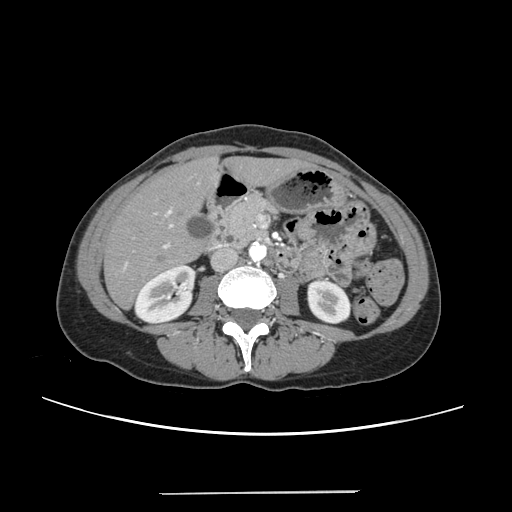
Contrast-enhanced abdominal CT, one axial slice. 120 kVp. Intravenous contrast given. Soft-tissue window (W 400 / L 40 HU). 512 × 512 image matrix, field of view 371 × 371 mm. Female patient, age 60 years. From the clinical record (not read from this slice): diagnosis: colorectal cancer liver metastases, imaged before liver resection; multiple liver metastases: no; largest metastasis: 1.5 cm; disease in both lobes: no.
Outlined on this slice (expert manual segmentation):
- liver: bounding box (x1, y1, x2, y2) in pixels: (106, 159, 300, 307)
- planned liver remnant (the part of the liver to remain after resection): (106, 160, 300, 307)
- portal vein (with intrahepatic branches): (123, 209, 173, 269)